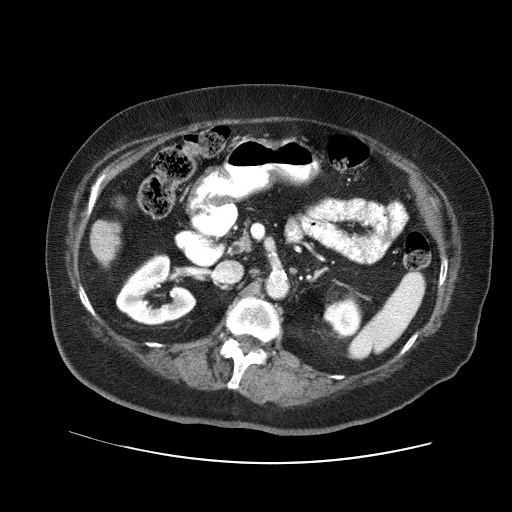
Contrast-enhanced abdominal CT (liver protocol), one axial slice. Slice 11 of 71 in the series (ordered by position). 120 kVp. Soft-tissue window (W 400 / L 40 HU). 512 × 512 image matrix, field of view 400 × 400 mm. Case-level facts recorded for this patient, not image findings: diagnosis: hepatocellular carcinoma (patient treated with transarterial chemoembolisation; whether this scan precedes or follows treatment is not stated here); TNM stage (as recorded): Stage-II.
Outlined on this slice (semi-automatically segmented with operator editing):
- liver parenchyma outside the tumour (the mass and vessels are separate outlines, so this box may not span the whole liver): bounding box <90,220,120,266> (left, top, right, bottom; pixels)